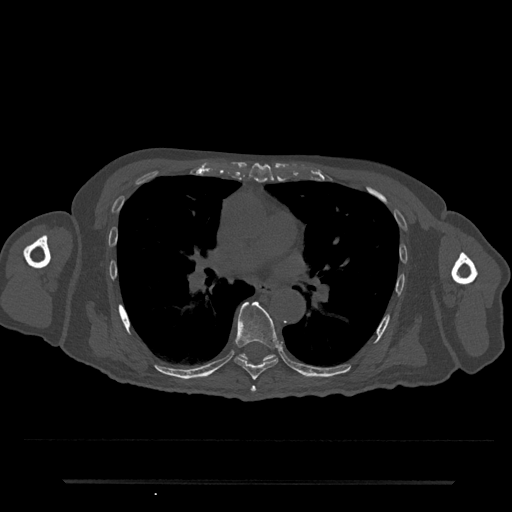
CT including the spine, one axial slice. Position 468 of 797 along the scan axis. Reconstruction kernel Br40s/3. 120 kVp. Bone window (W 1800 / L 400 HU). 512 × 512 image matrix, field of view 427 × 427 mm. Patient: male, 74 years. Case-level facts recorded for this patient, not image findings: primary cancer: prostate.
Annotated regions visible in this slice (semi-automatically segmented with operator editing):
- T6 vertebra: bounding box (x1, y1, x2, y2) in pixels: (250, 386, 256, 392)
- T7 vertebra: (234, 301, 279, 380)
- T8 vertebra: (240, 353, 276, 361)